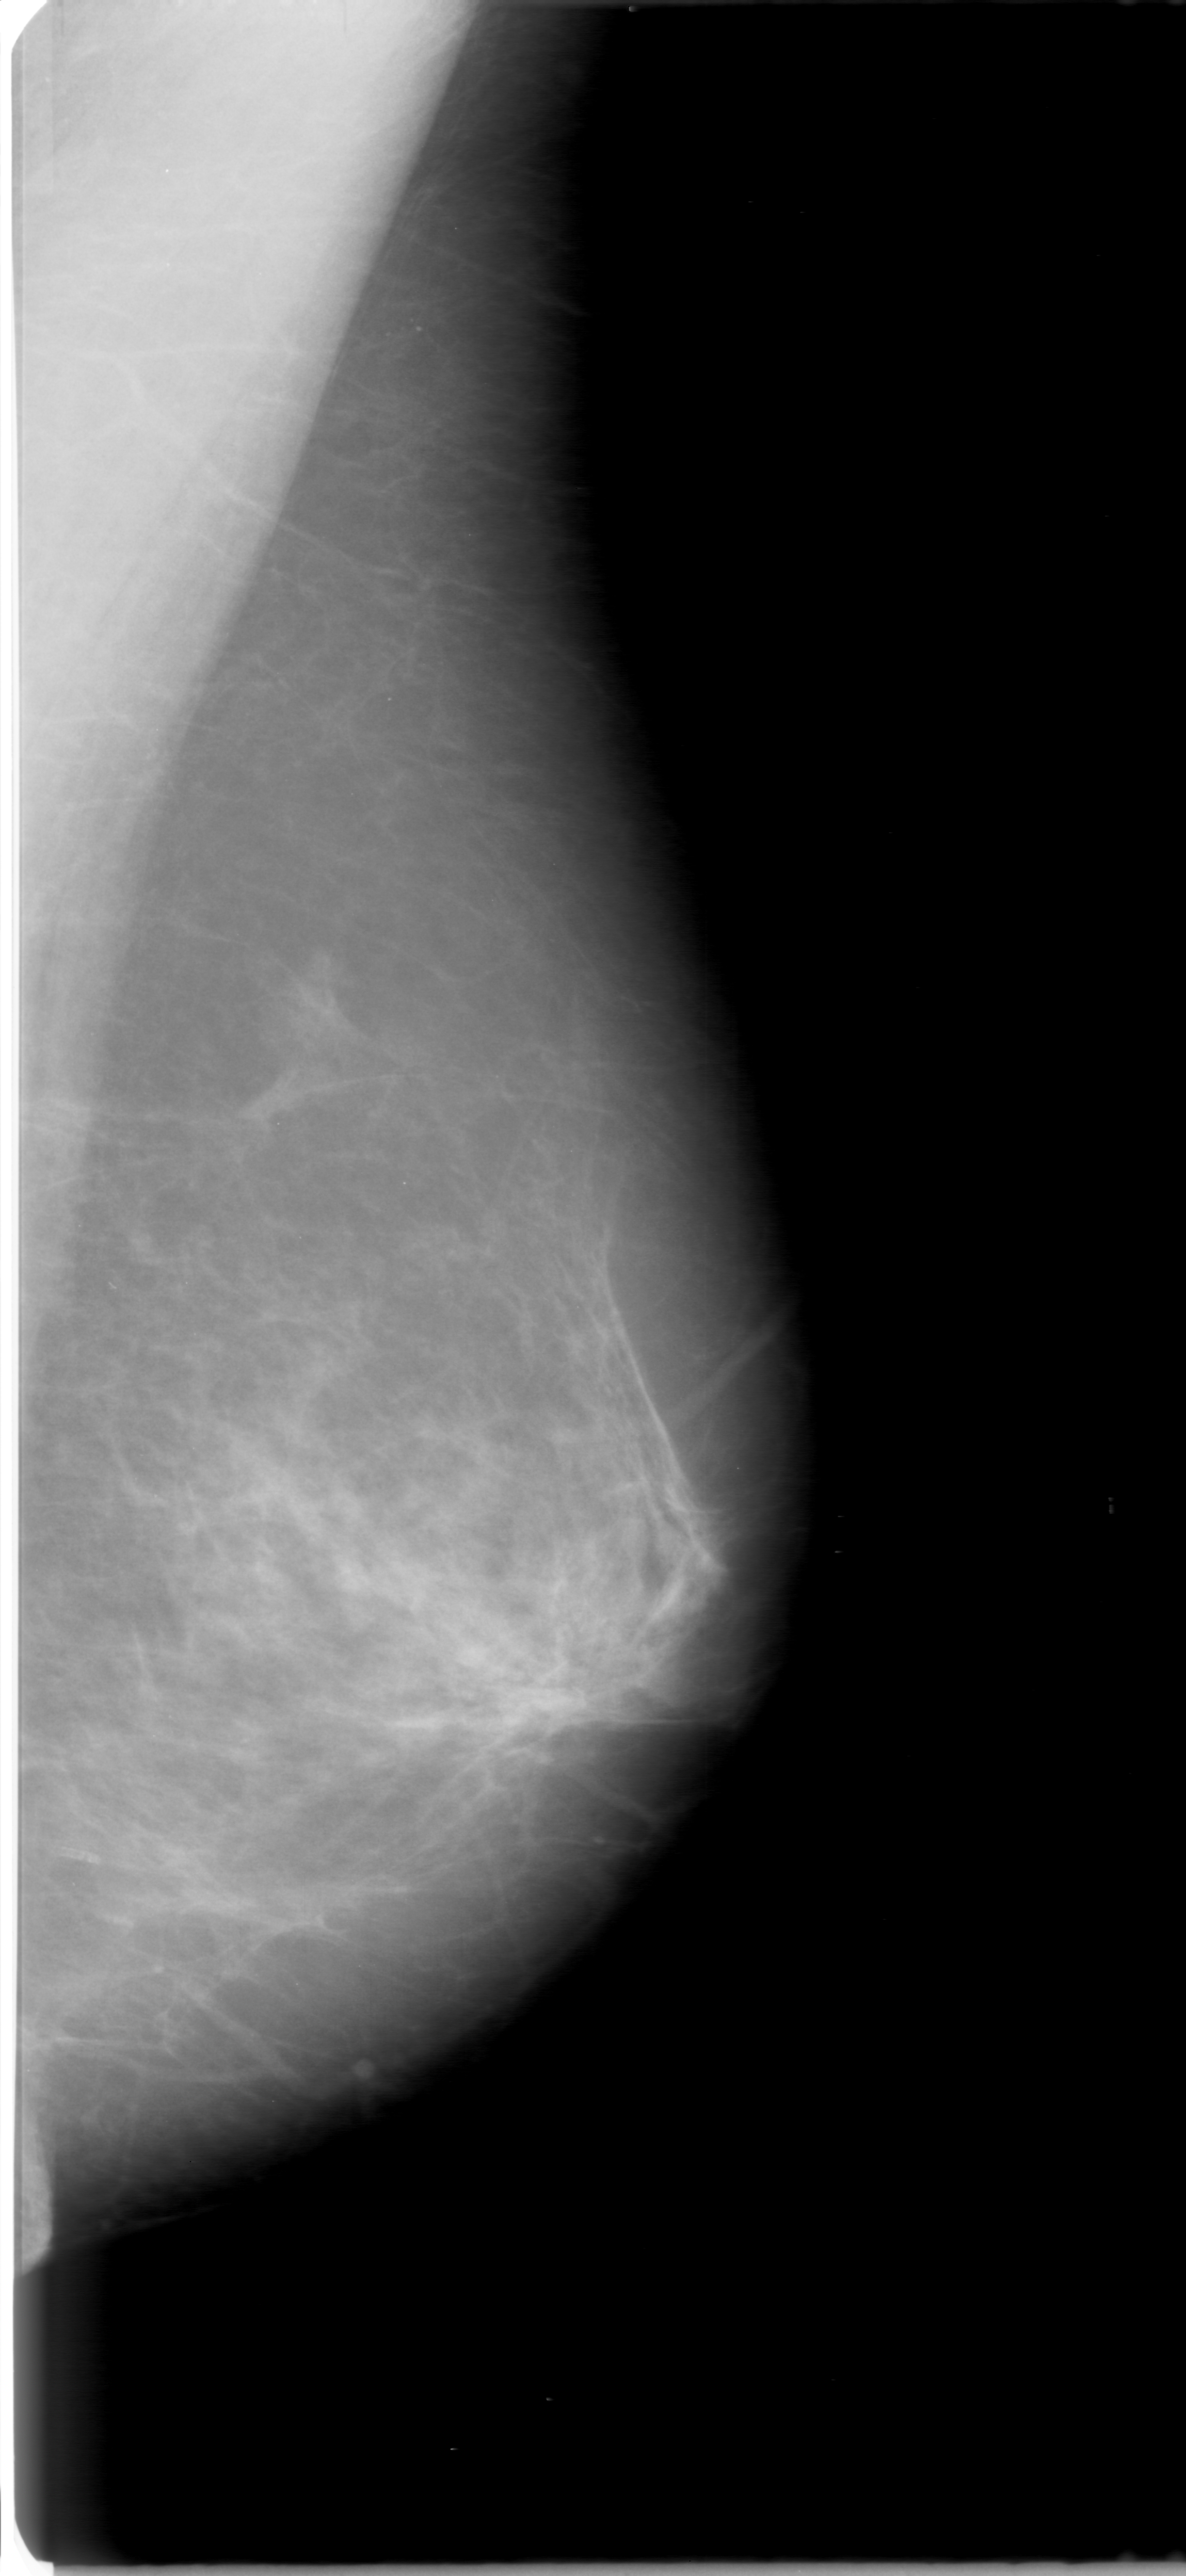
Digitized screen-film mammogram. Left breast. MLO view. 1186 × 2576 image matrix.
Expert-marked regions of interest on this film, with their recorded descriptors:
- mass, shape irregular, margins ill defined; BI-RADS assessment category 2; pathology (as recorded): benign: bounding box (x1, y1, x2, y2) in pixels: (250, 943, 377, 1115)